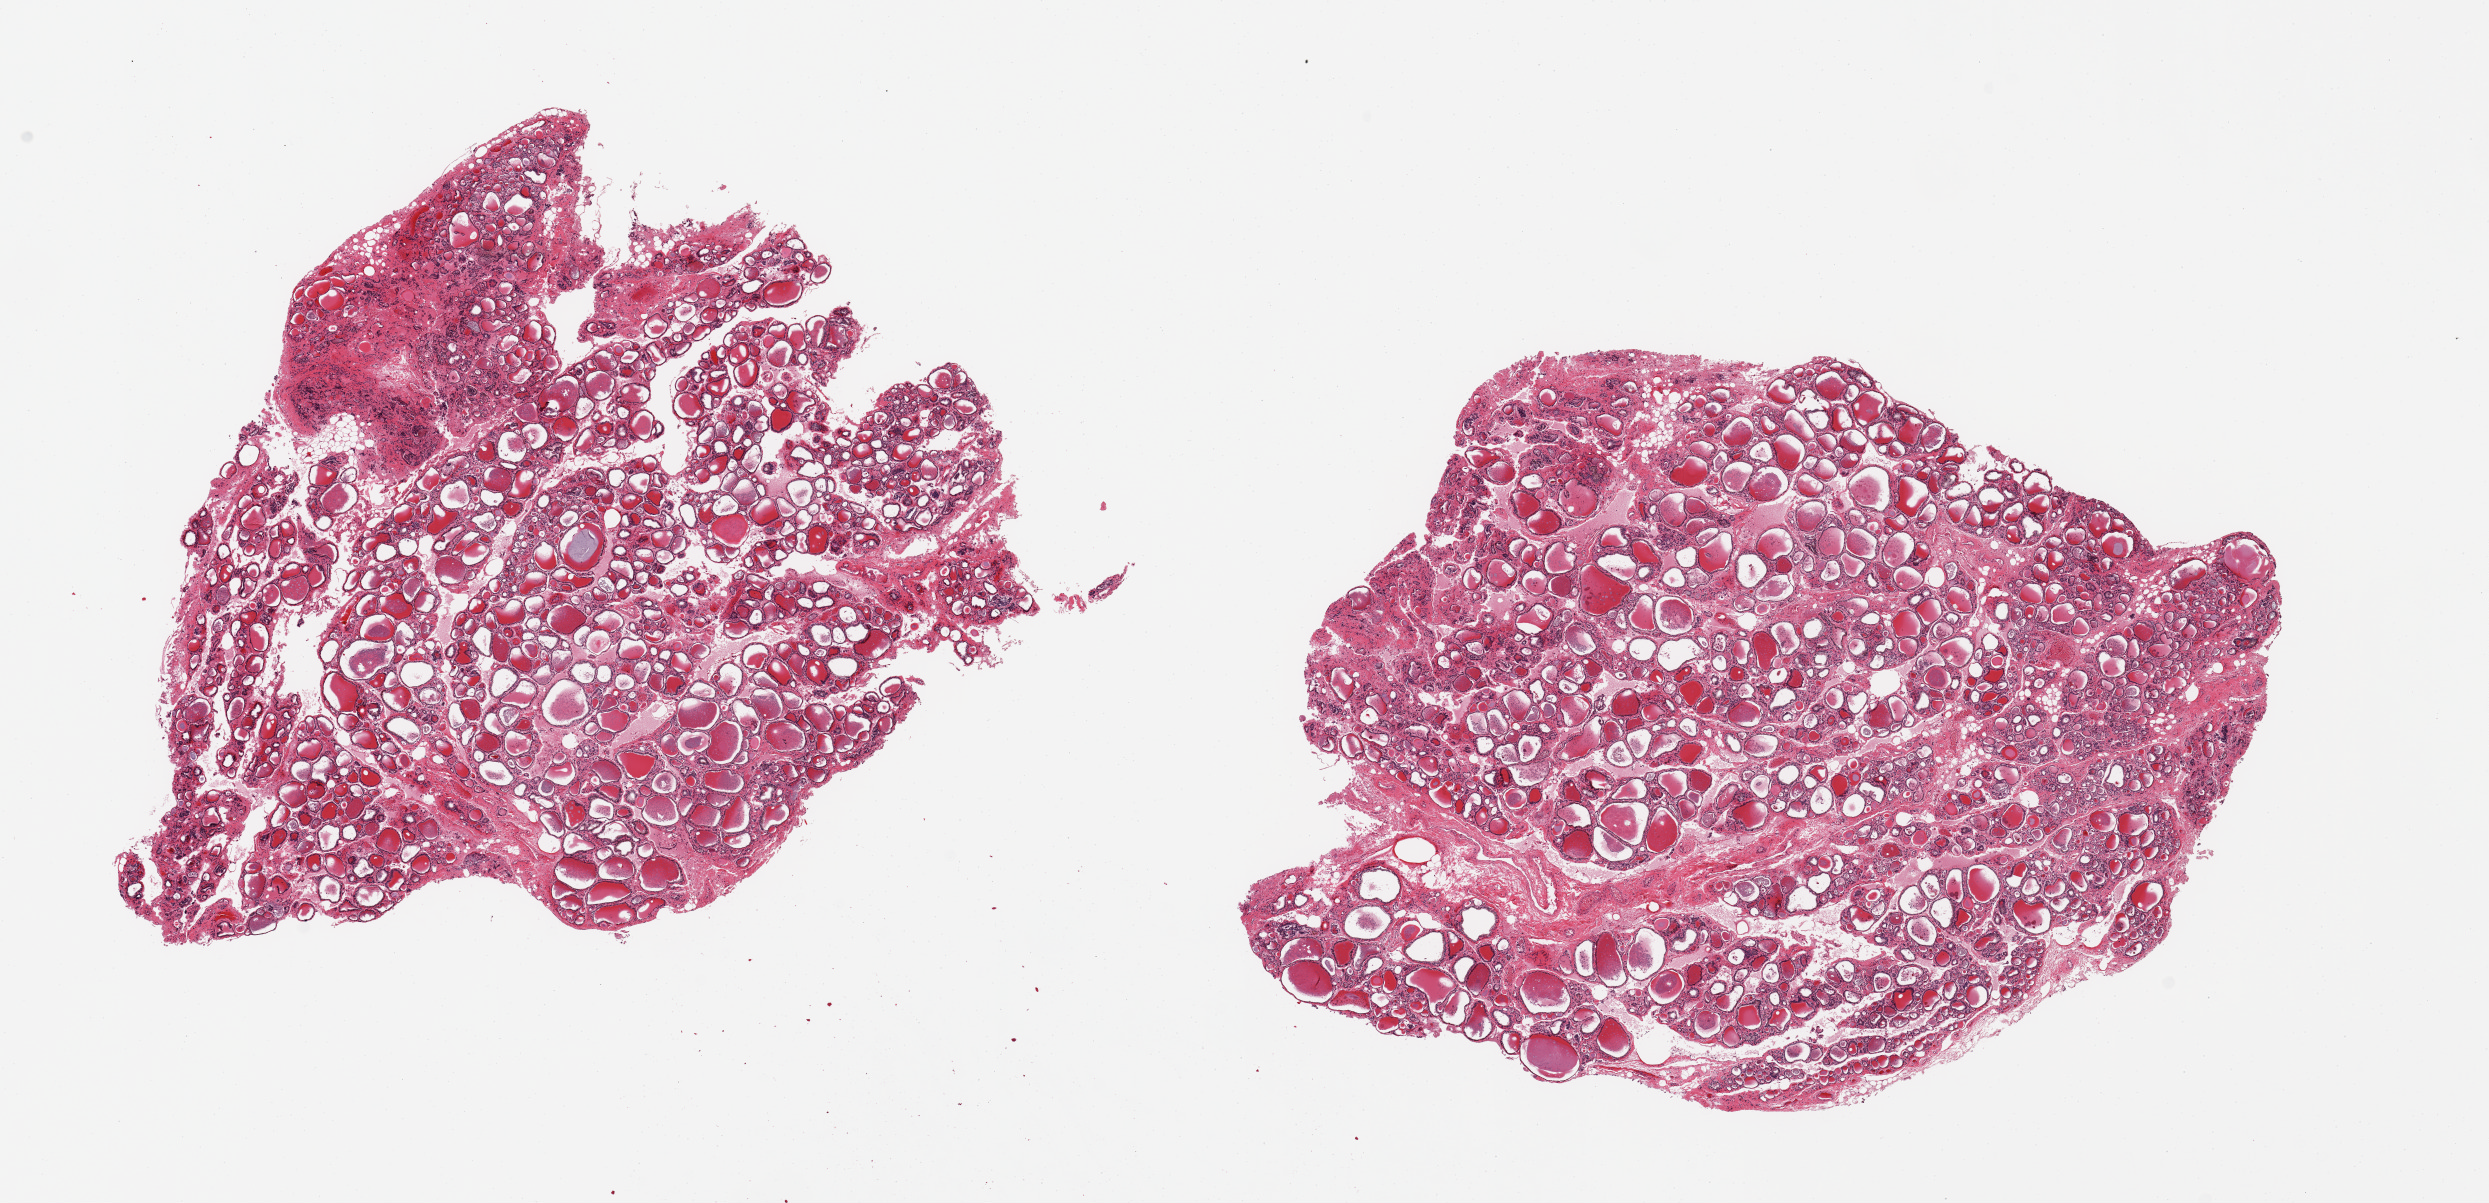
Digitized haematoxylin and eosin-stained section, brightfield, whole scanned area (about 19.7 x 9.5 mm, from a 20x scan) shown as a low-resolution overview, PAXgene-fixed, paraffin-embedded tissue, sampled site (target tissue): thyroid, donor tissue sample. Donor: male.
Review note (as recorded): 2 pieces, mild regressive changes.